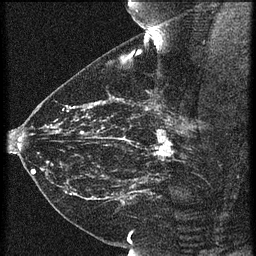
Breast MRI (dynamic contrast-enhanced), one sagittal slice; slice 40 of 60 in the series (ordered by position); 3 images stored at this slice position (order not interpretable as contrast timing); 1.5 T; TE 4.2 ms, TR 21.3 ms; 1.5 mm slice thickness; 256 × 256 image matrix. Patient: female, 43 years. Case-level facts recorded for this patient, not image findings: setting: breast cancer imaged before/during neoadjuvant chemotherapy; receptor status: HER2-positive.
Annotated regions visible in this slice (semi-automatically segmented with operator editing):
- analysis volume of interest (the breast-tissue region the enhancement analysis was run in; not a lesion): box from (x=119, y=114) to (x=189, y=173) px
- tumour enhancement mask (voxels above the 90 % enhancement threshold inside the analysis volume of interest): (x=153, y=130)–(x=173, y=161)